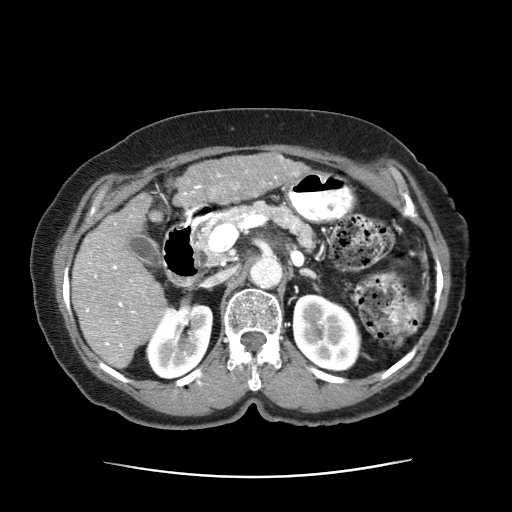
Contrast-enhanced abdominal CT (liver protocol), one axial slice. Position 23 of 63 along the scan axis. 120 kVp. Soft-tissue window (W 400 / L 40 HU). 2.5 mm slice thickness. 512 × 512 image matrix. Patient: female, 79 years. Case-level facts recorded for this patient, not image findings: diagnosis: hepatocellular carcinoma (patient treated with transarterial chemoembolisation; whether this scan precedes or follows treatment is not stated here); TNM stage (as recorded): Stage-II; Child-Pugh class: B; tumour differentiation: well differentiated; tumour nodularity: multinodular.
Outlined on this slice (semi-automatic segmentation, software-assisted and operator-edited):
- abdominal aorta: bounding box (x1, y1, x2, y2) in pixels: (250, 251, 283, 287)
- liver parenchyma outside the tumour (the mass and vessels are separate outlines, so this box may not span the whole liver): (72, 195, 167, 371)
- mass: (175, 152, 306, 204)
- liver vessels: (85, 176, 277, 347)